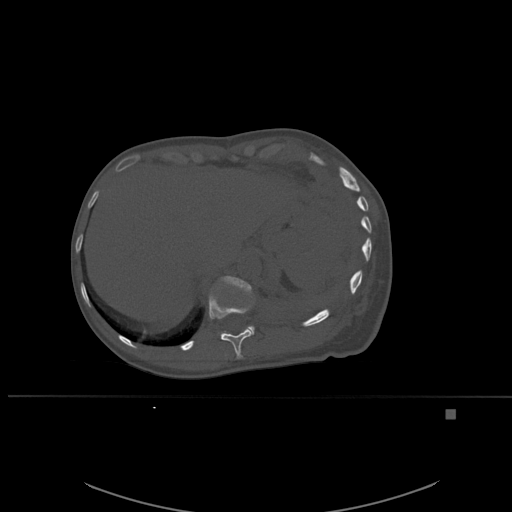
CT including the spine, one axial slice; bone window (W 1800 / L 400 HU); 1.5 mm slice thickness; 512 × 512 image matrix, field of view 440 × 440 mm. Female patient, age 45 years. Case-level facts recorded for this patient, not image findings: primary cancer: lung.
Outlined on this slice (semi-automatically segmented with operator editing):
- T11 vertebra: box from (x=209, y=289) to (x=254, y=359) px
- T12 vertebra: (x=216, y=276)–(x=255, y=332)